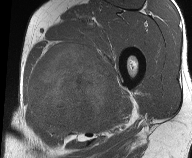
MRI of an extremity soft-tissue mass, one axial slice. Slice 32 of 61 in the series (ordered by position). MR volume resampled by the dataset authors to the PET/CT grid (not the native acquisition matrix). 3.27 mm slice thickness. 192 × 158 image matrix, field of view 187 × 154 mm. Male patient. From the clinical record (not read from this slice): histological type: pleiomorphic liposarcoma; grade: high; site of the primary tumour: left thigh.
Structures marked on this image (expert contour drawn on MRI and transferred to this co-registered scan by the dataset authors):
- gross tumour volume including surrounding oedema: bounding box <27,41,122,136> (left, top, right, bottom; pixels)
- gross tumour volume (mass): <29,43,120,129>